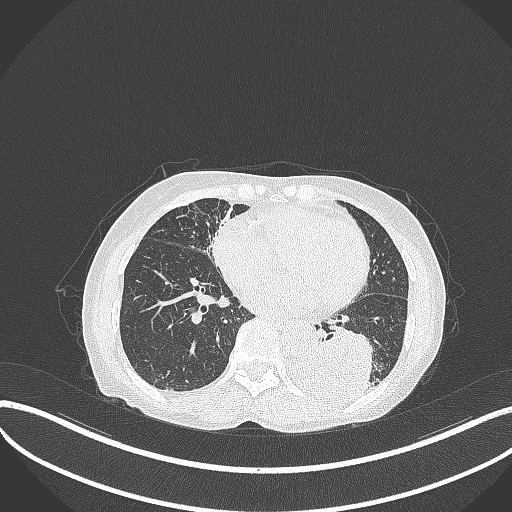
Chest CT, one axial slice; slice 113 of 370 in the series (ordered by position); reconstruction kernel B70f; 120 kVp; lung window (W 1500 / L -600 HU); 1 mm slice thickness; 512 × 512 image matrix, field of view 400 × 400 mm. Patient: female, 78 years. From the clinical record (not read from this slice): clinical TNM (as recorded): T3 N0 M1.
Annotated regions visible in this slice (rectangle marked by the reading radiologist):
- lung tumour (recorded histology: squamous cell carcinoma): box from (x=281, y=325) to (x=374, y=409) px